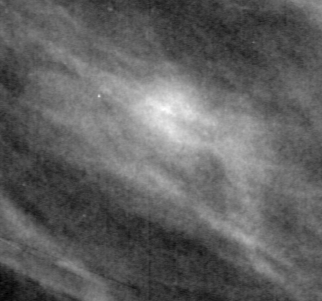
Crop from a digitized film mammogram around one marked abnormality; right breast; MLO view.
Mass, shape oval, margins circumscribed; BI-RADS assessment category 4; subtlety rating 3 on a 1 (subtle) to 5 (obvious) scale; pathology result (as recorded, not read from the image): benign.